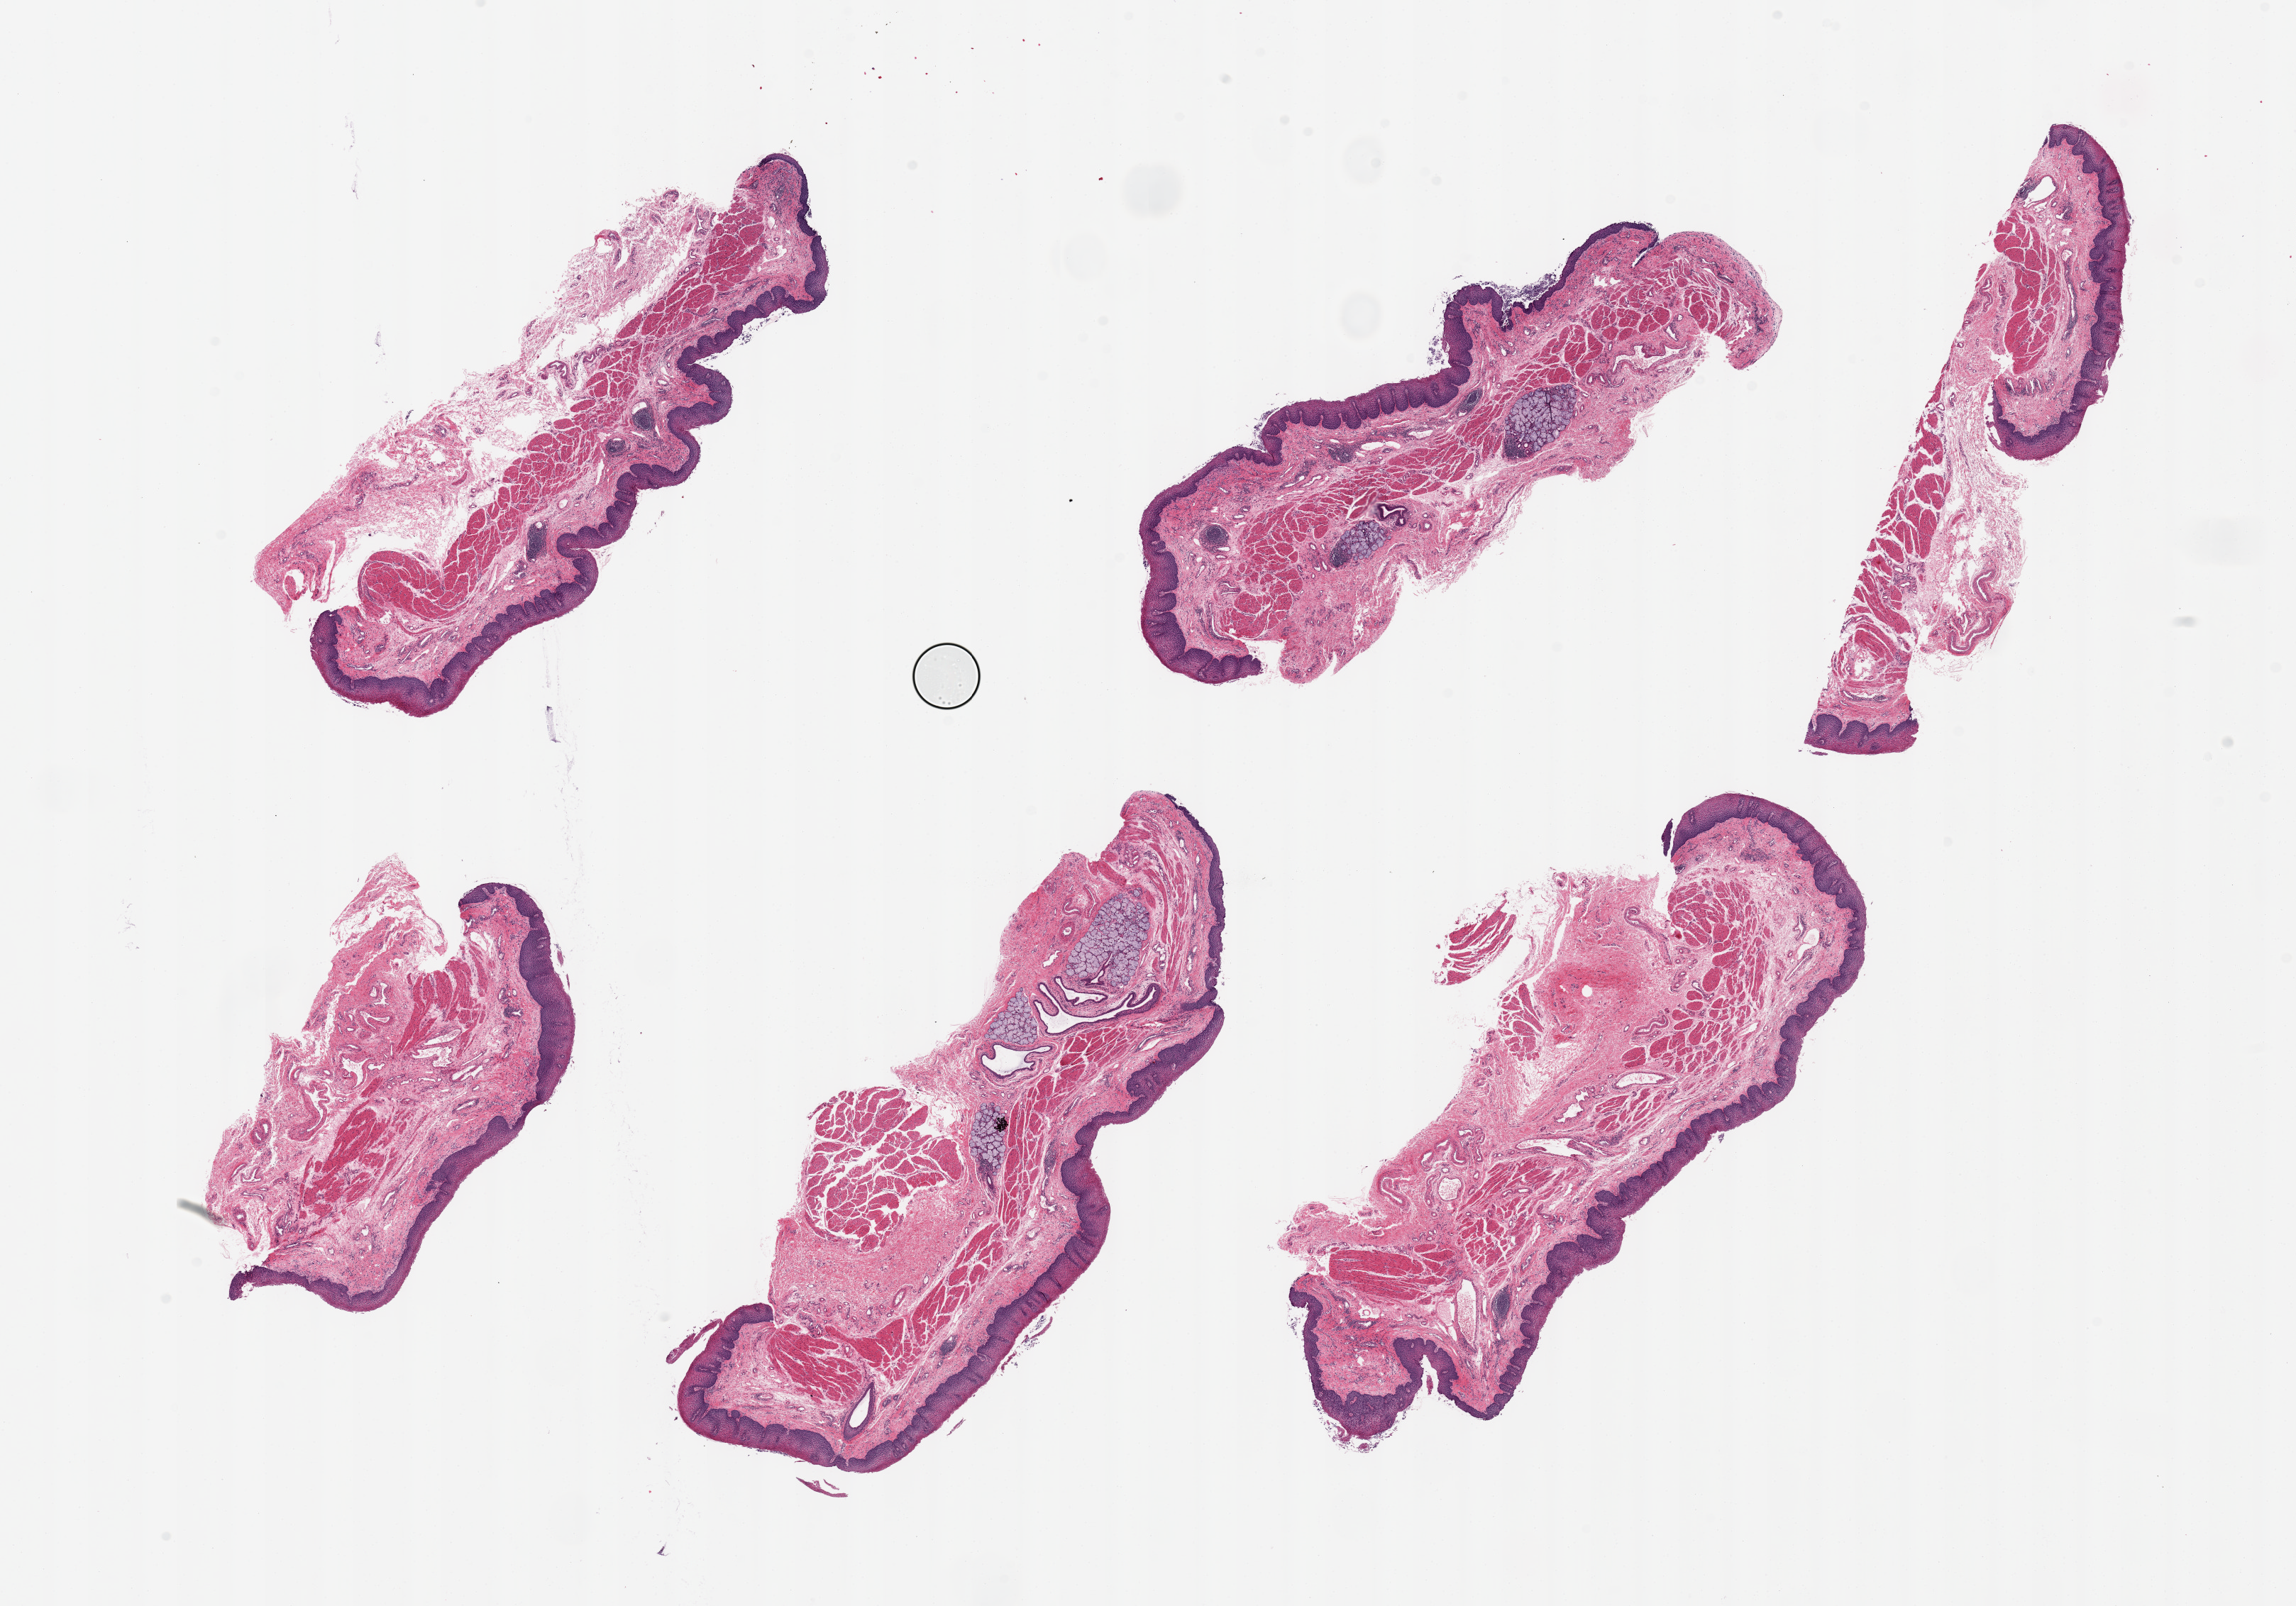
Digitized haematoxylin and eosin-stained section, brightfield, a low-resolution overview of the entire scanned area, about 25.6 x 17.9 mm (slide scanned at 20x), PAXgene-fixed paraffin-embedded (PFPE) section, target tissue: esophageal mucous membrane, tissue donor sample. Donor: male.
Pathologist's review note for this sample: 6 pieces, up to 8x4mm; ~10-15% thickness is wel preserved squamous mucosa; sub-mucosal mucus glands present.